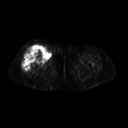
FDG PET of an extremity soft-tissue mass (from a PET/CT study), one axial slice. Position 253 of 311 along the scan axis. 128 × 128 image matrix, field of view 500 × 500 mm. Patient: female, 57 years. Case-level facts recorded for this patient, not image findings: histological type: pleiomorphic undifferentiated sarcoma; grade: high; site of the primary tumour: right quadricep.
Structures marked on this image (expert contour drawn on MRI and transferred to this co-registered scan by the dataset authors):
- tumour plus oedema (research contour): bounding box (x1, y1, x2, y2) in pixels: (22, 45, 50, 72)
- tumour (research contour): (22, 45, 50, 72)